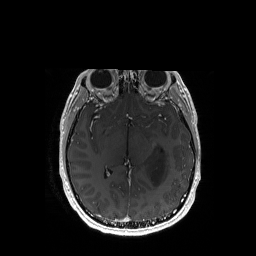
Brain MRI from a brain-tumour surgery series, one axial slice. Position 95 of 192 along the scan axis. T1-weighted post-contrast. 1 mm slice thickness. 256 × 256 image matrix, field of view 256 × 256 mm. From the clinical record (not read from this slice): histopathology: Astrocytoma; WHO grade: 3; IDH mutation: yes; tumour location: Left Temporal.
Outlined on this slice (expert manual segmentation):
- tumour: box from (x=148, y=146) to (x=167, y=185) px